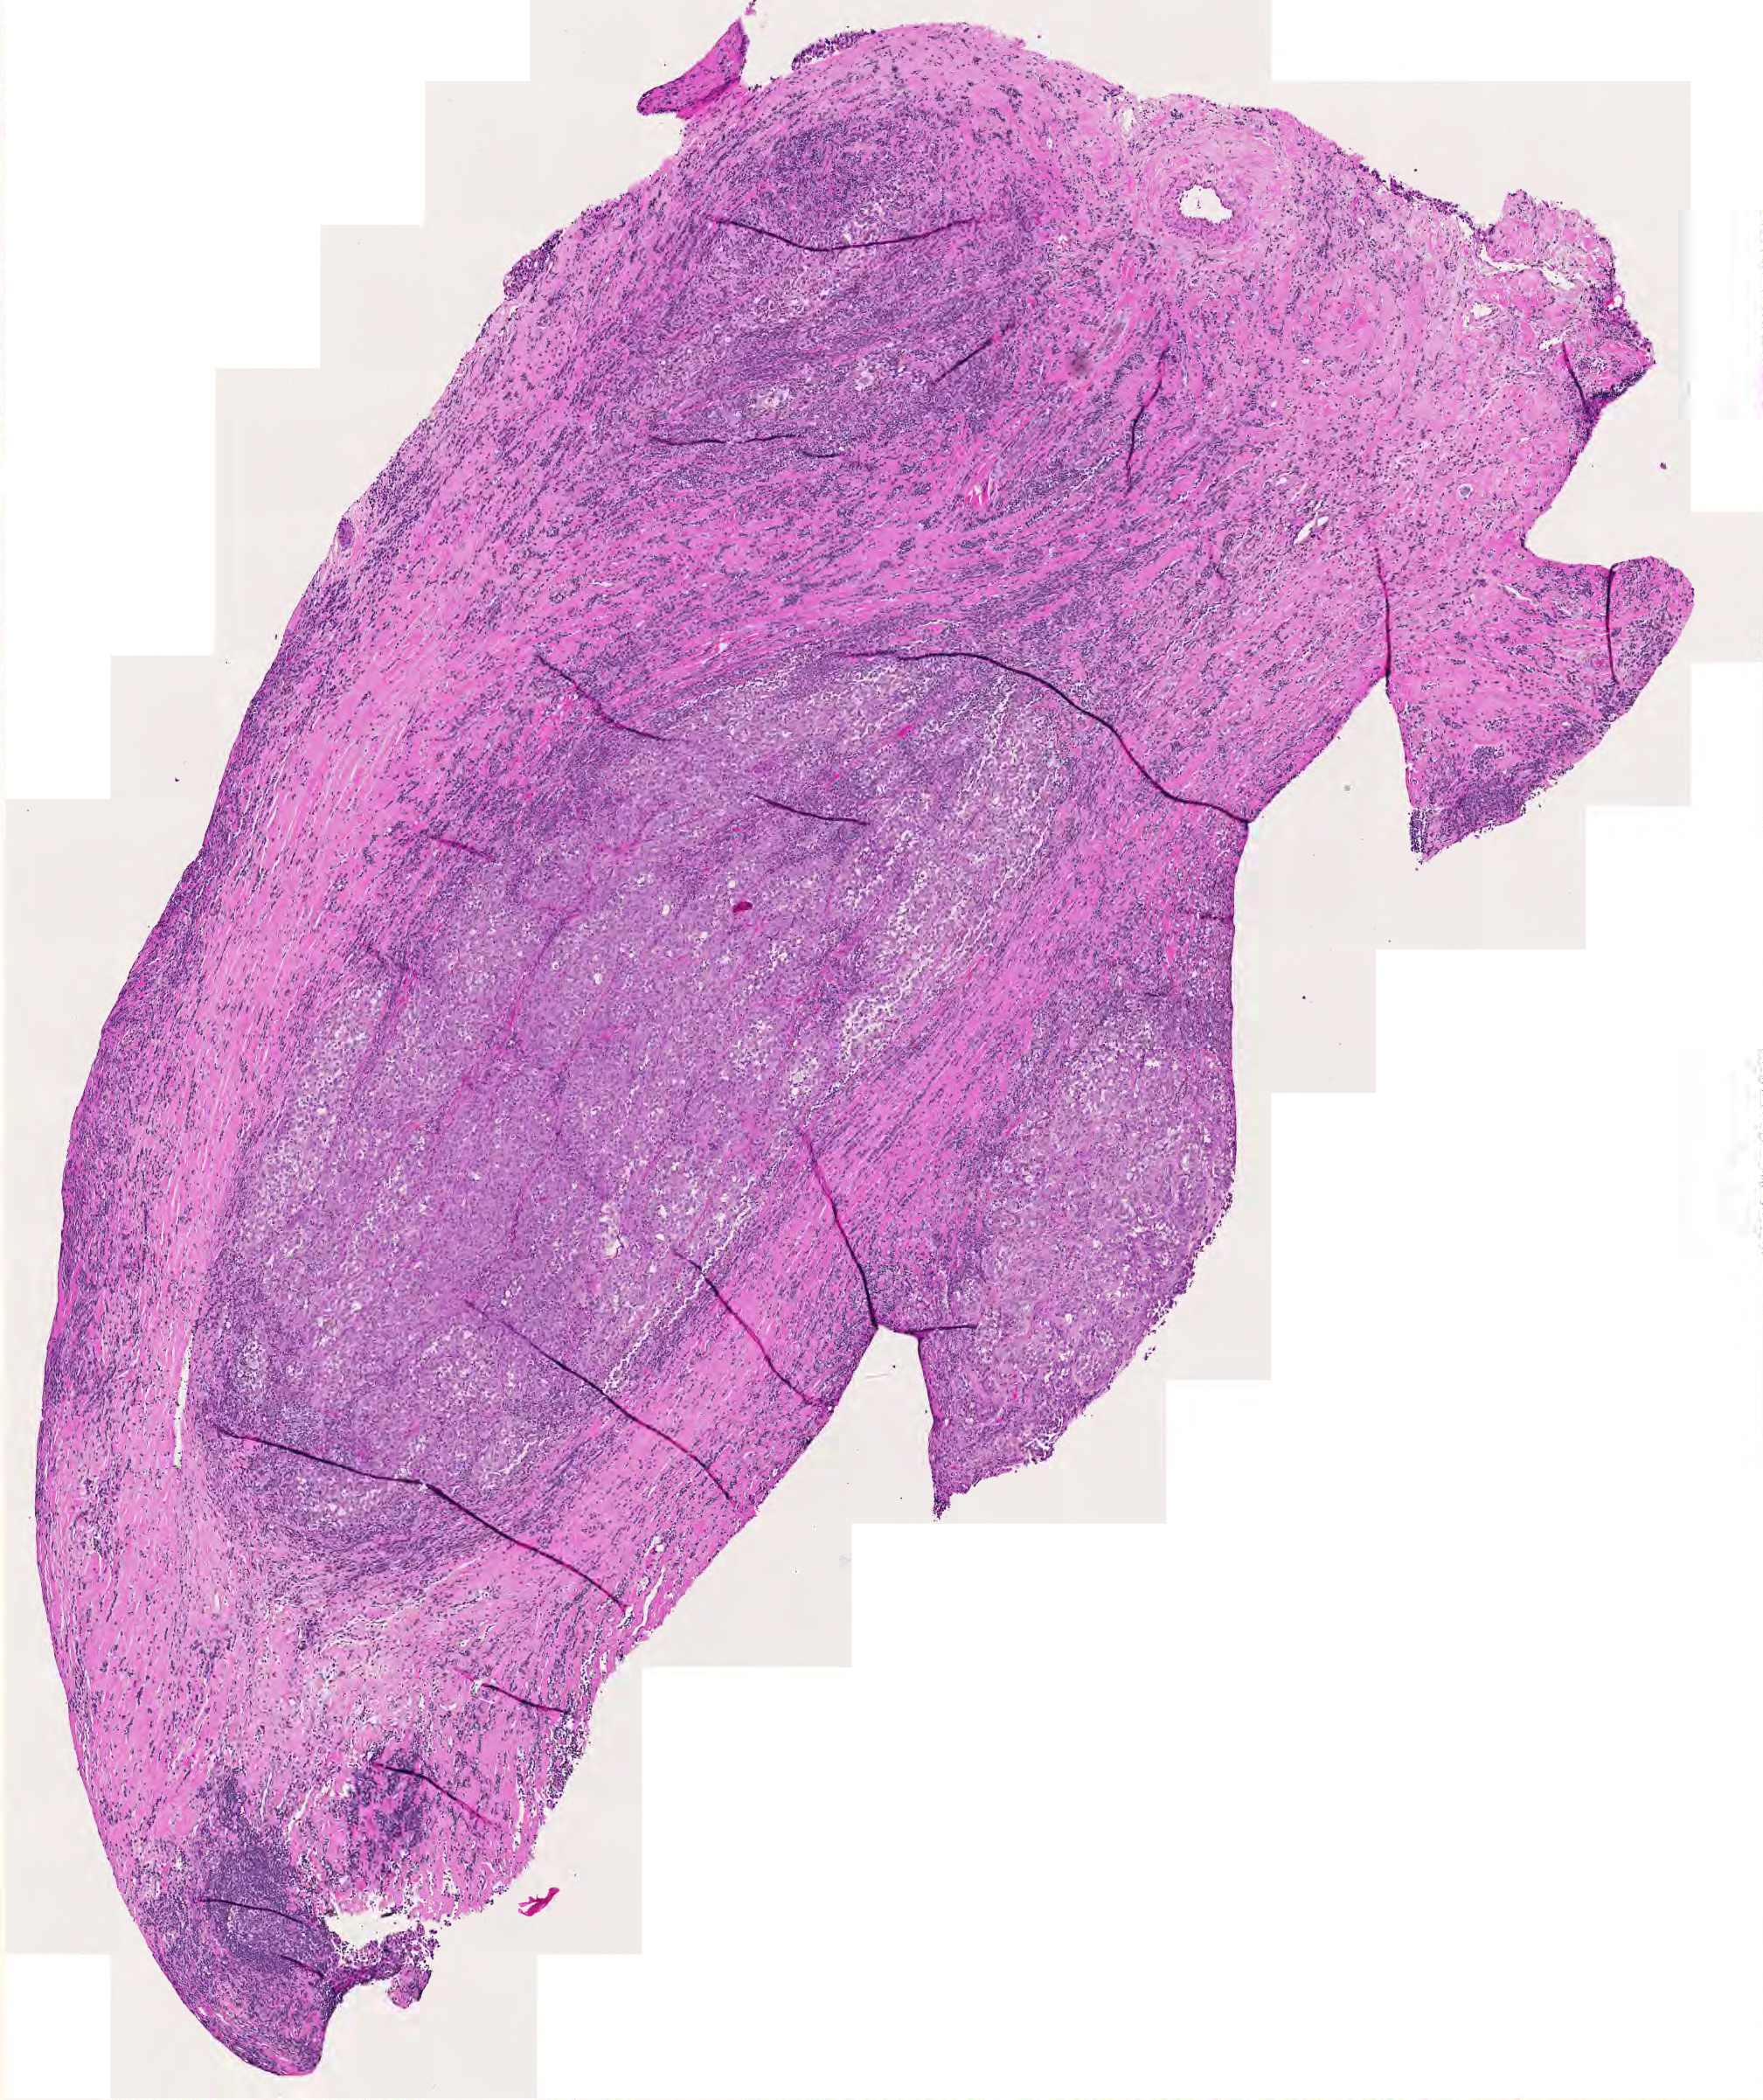
Whole-slide histology image, Hematoxylin and eosin (H&E) stained — a low-resolution overview of the entire scanned area, about 5.2 x 6.2 mm. Melanoma tumour tissue; sampled site not recorded. Patient: male, age 68 years.
- AJCC pathologic stage: 0
- diagnosis: Malignant melanoma, NOS